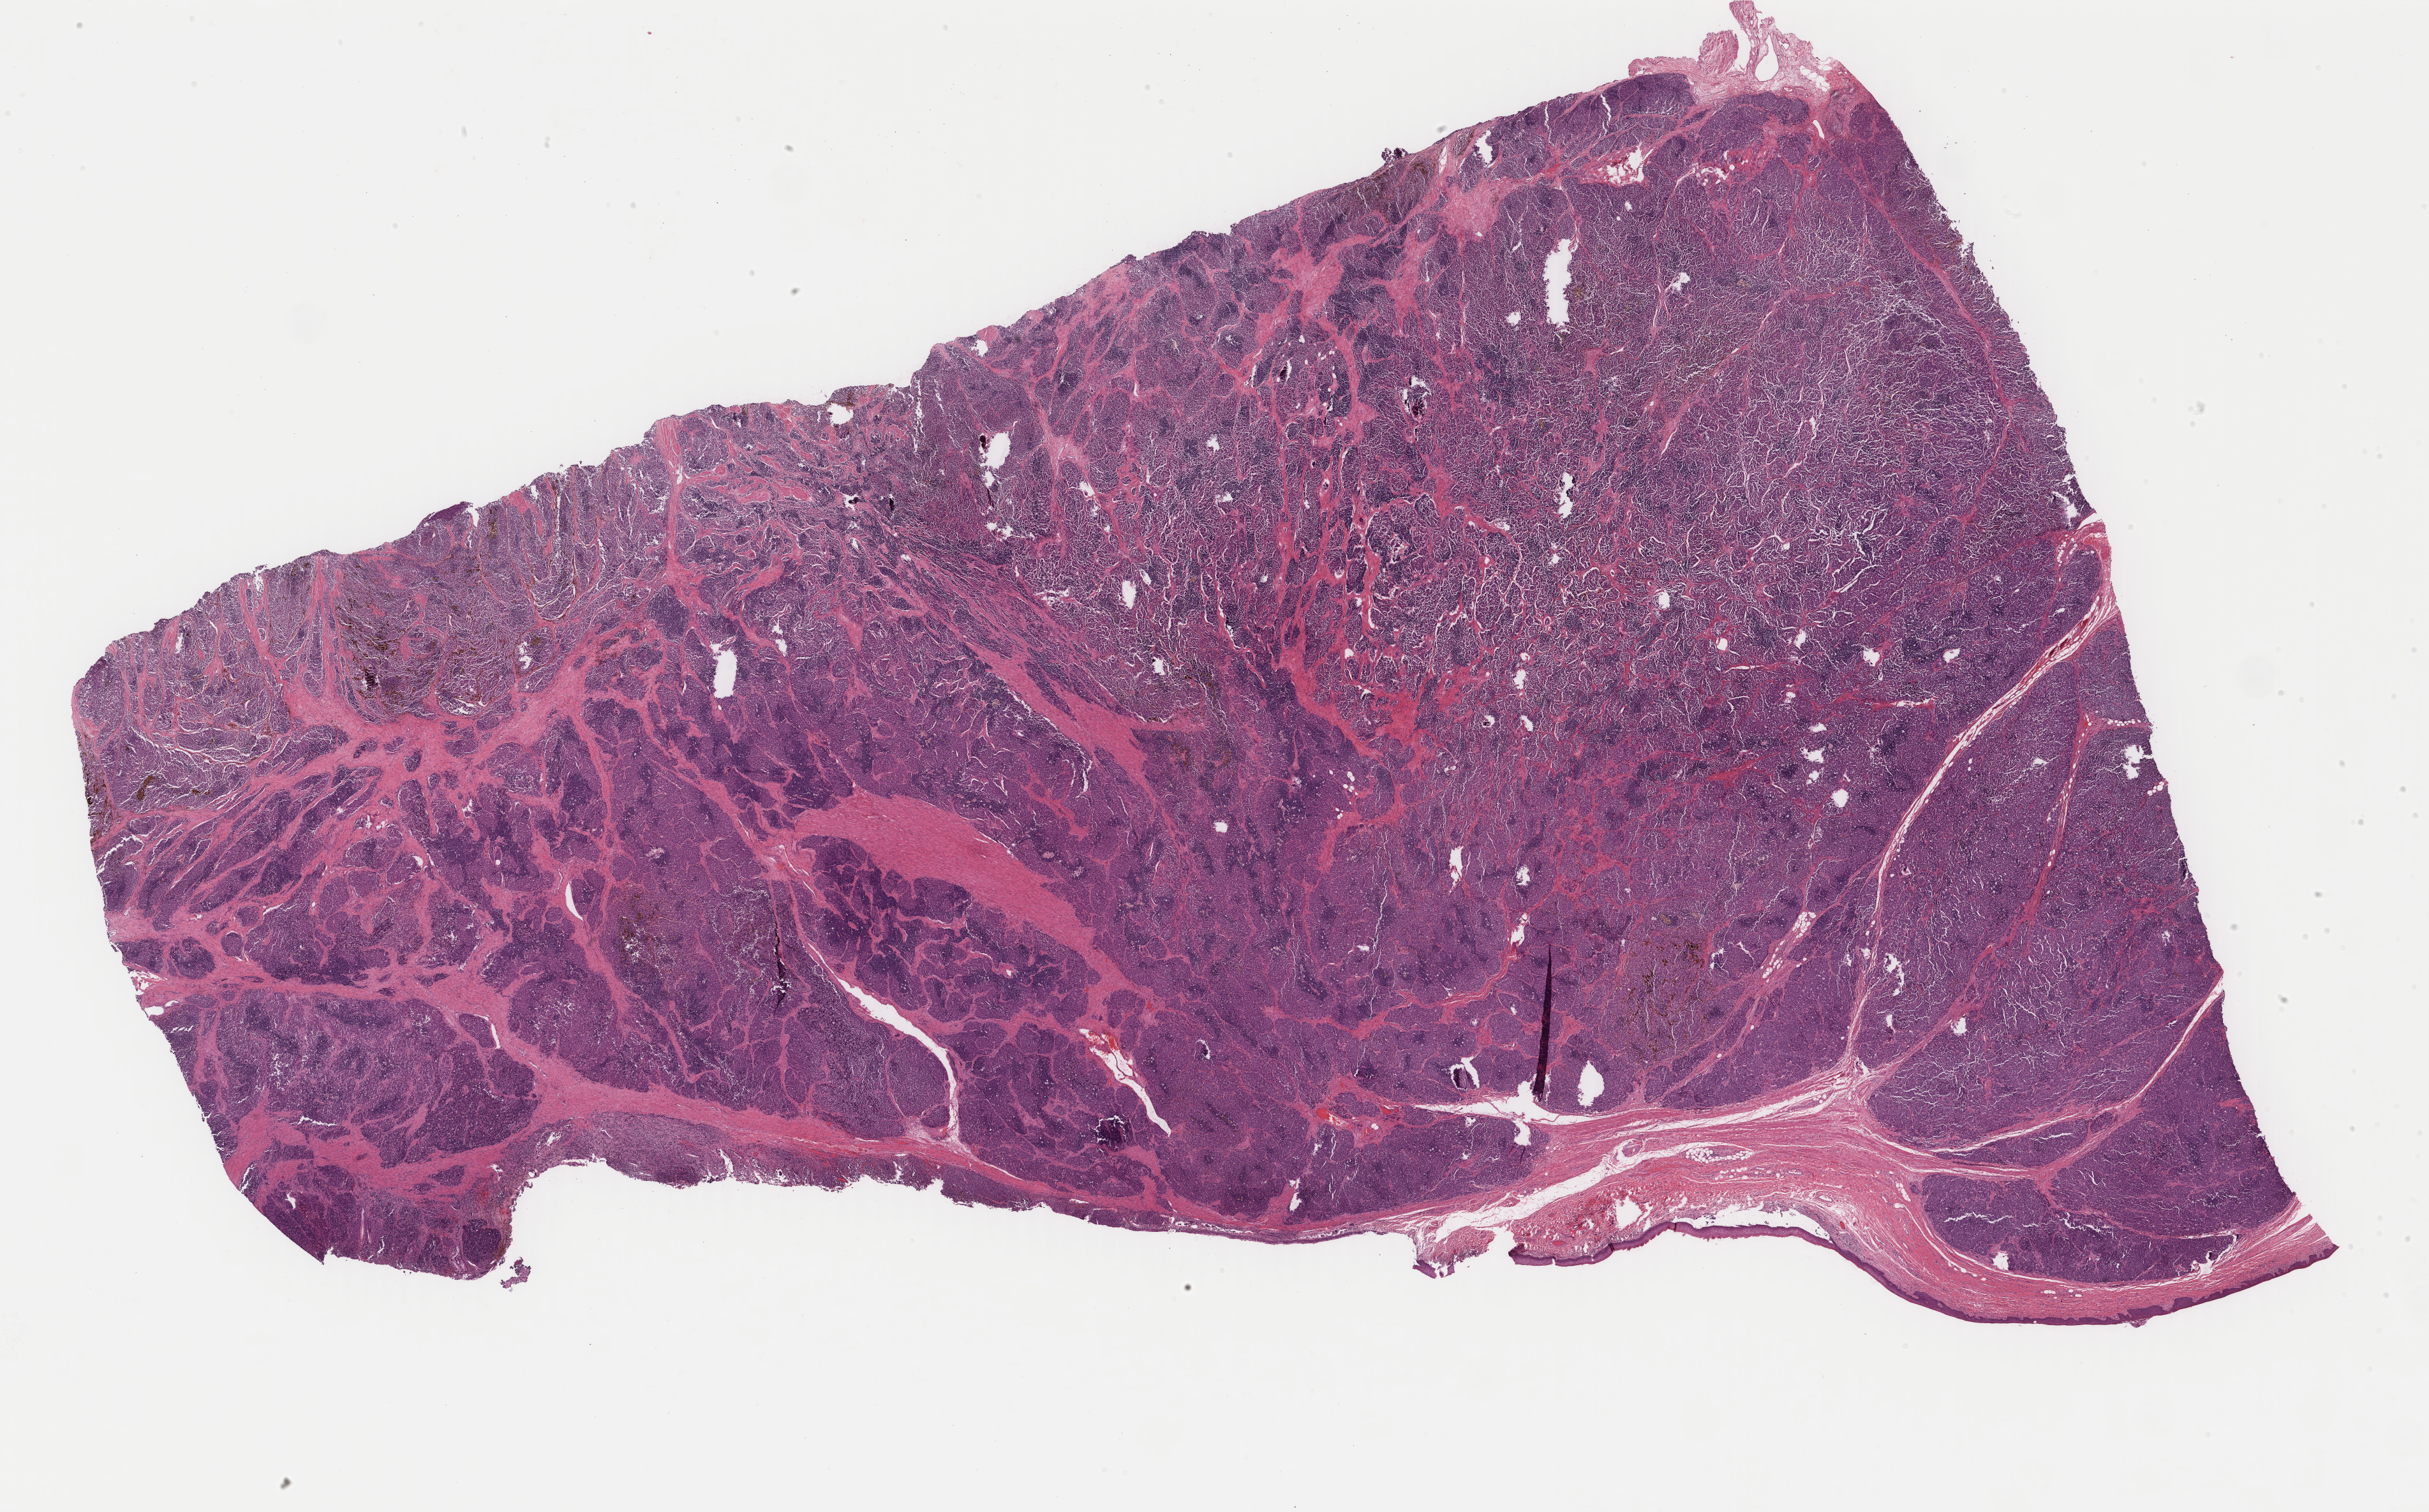
Whole-slide histology image, Hematoxylin and eosin (H&E) stained, shown as a low-resolution overview of the whole scanned area (about 30.2 x 18.8 mm); FFPE section; primary tumour sample from the skin. Patient: male, age at initial diagnosis 76 years.
Diagnosis: Malignant melanoma, NOS.